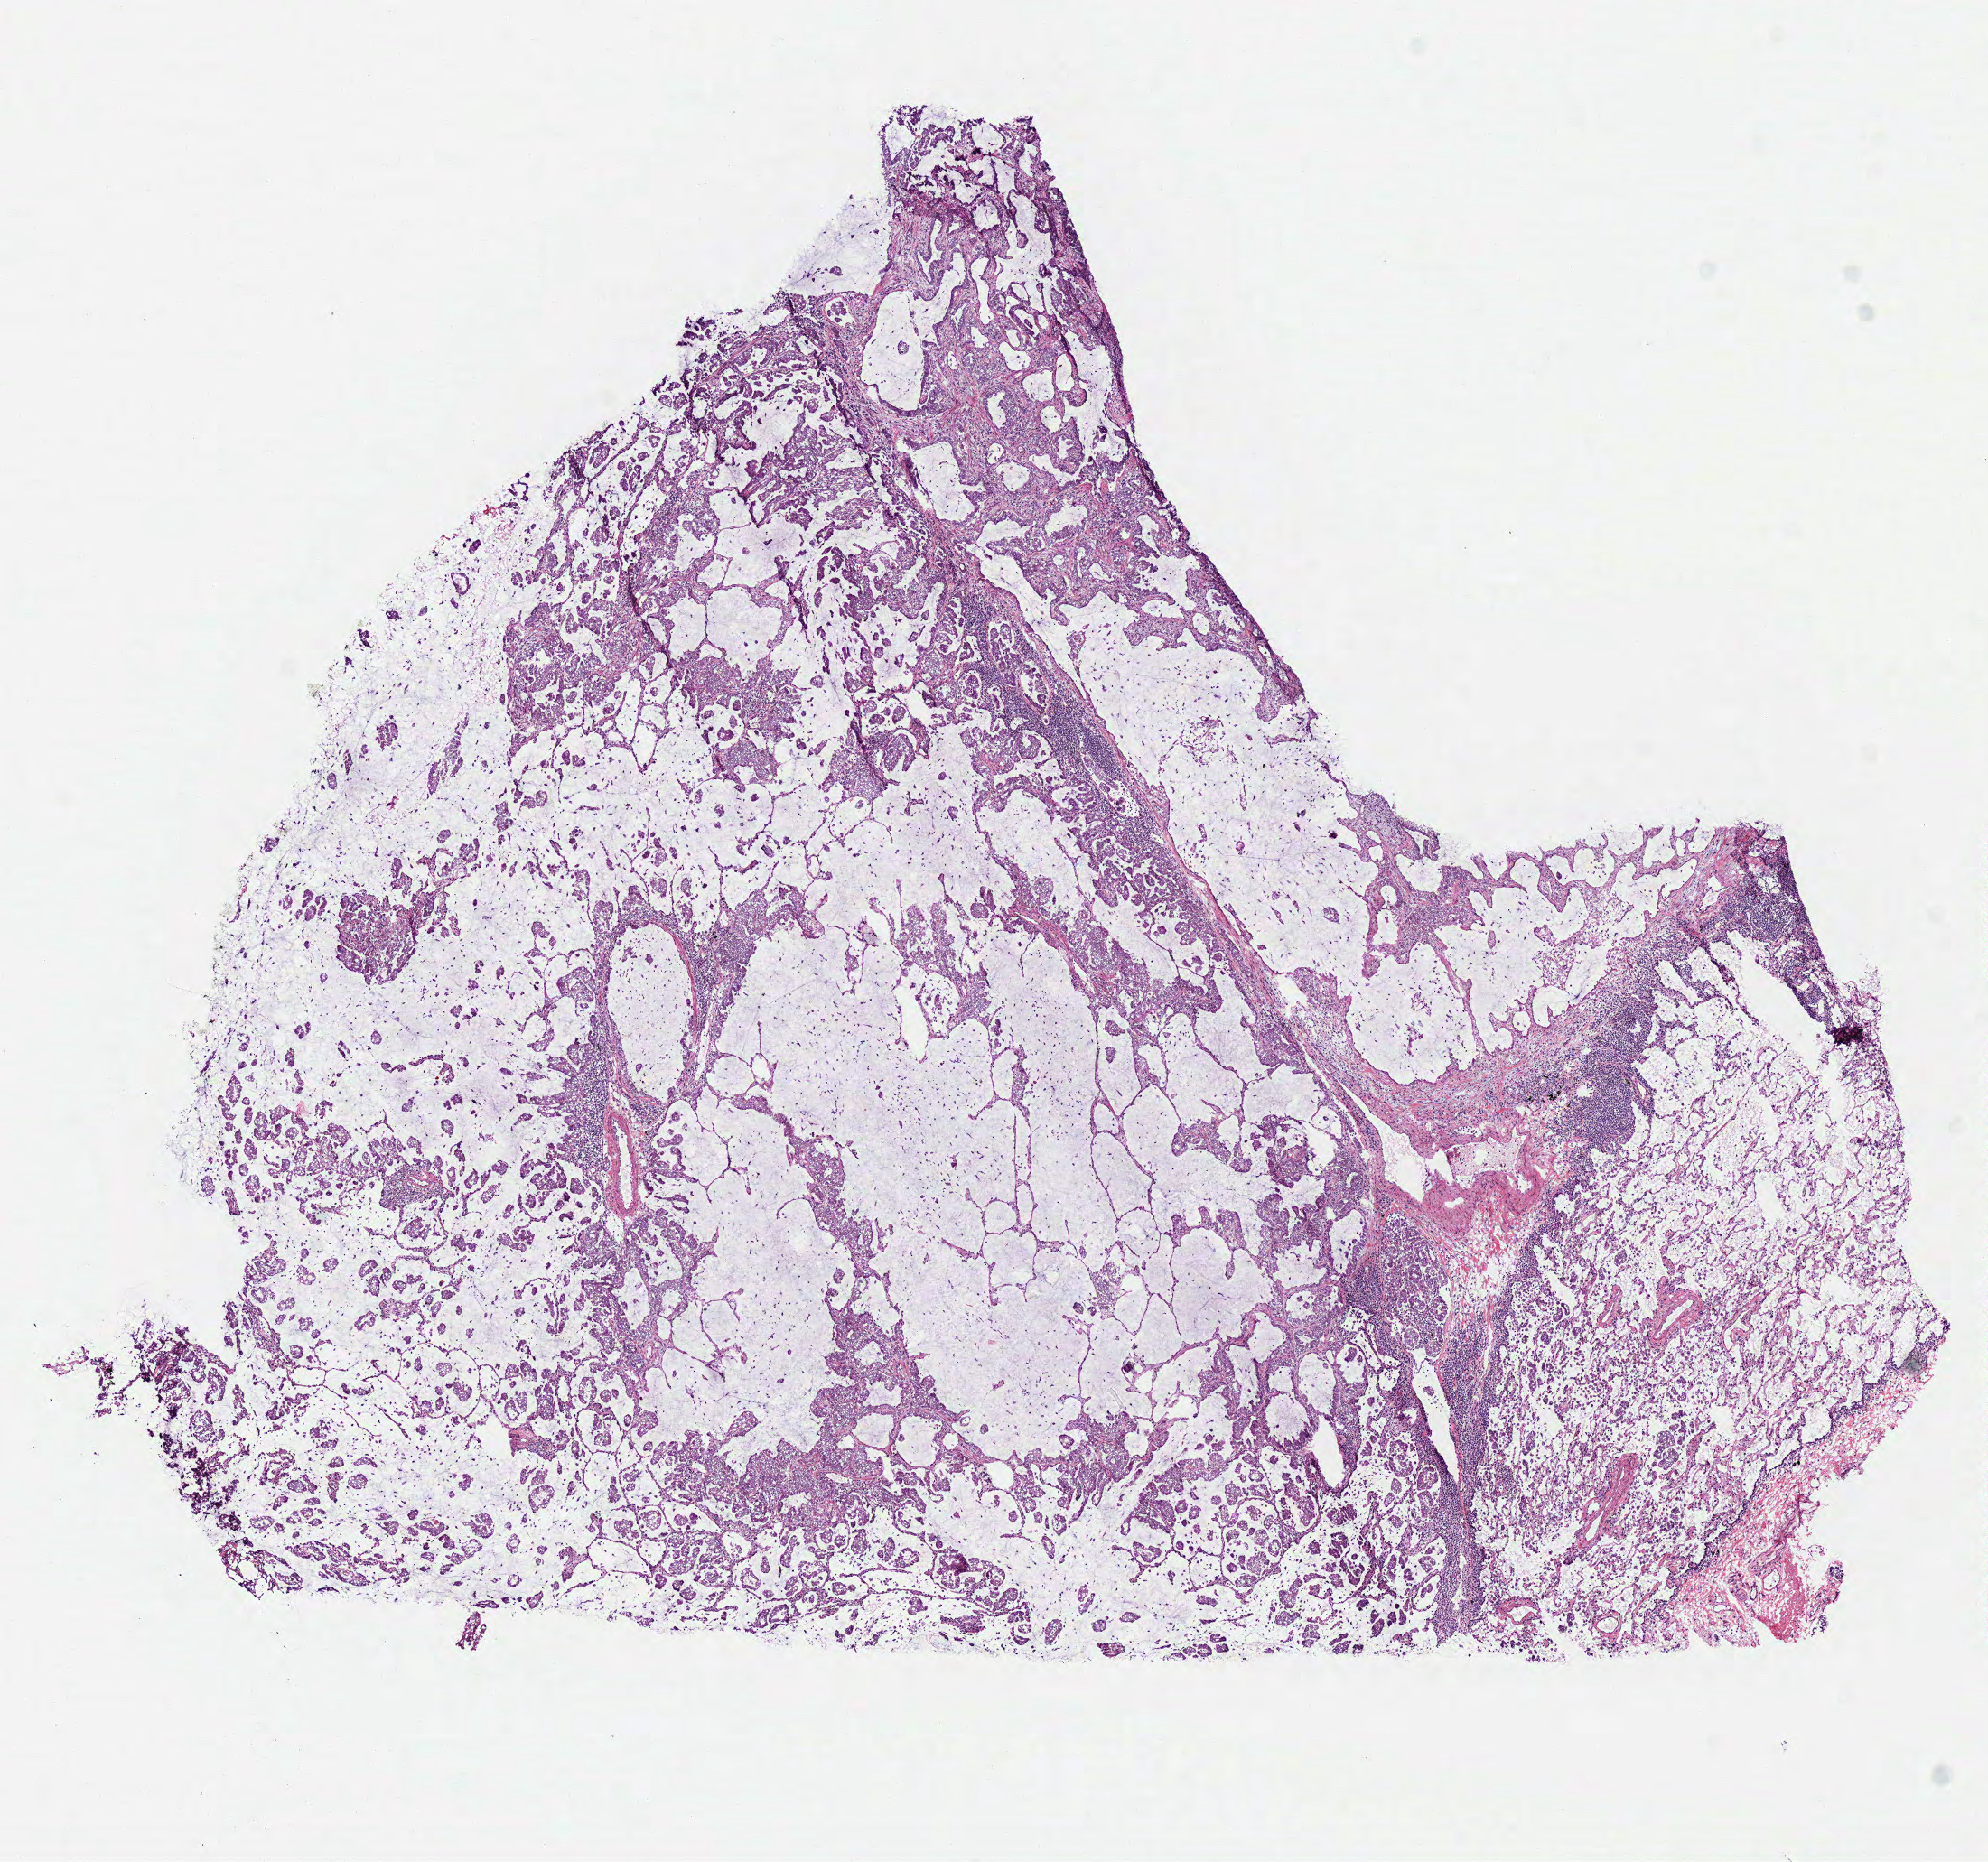
Whole-slide histology image, H&E-stained — low-resolution overview of the scanned area, about 8.7 x 8.1 mm. Frozen section from the bottom of the tissue portion. Lung, primary tumour sample. Male, age 61 years at initial diagnosis. Pathologist review of this section (percent, as recorded): tumour cells 85%, tumour nuclei 60%, normal cells 0%, stromal cells 15%, necrosis 0%.
AJCC pathologic stage: IV. Laterality: right. Pathologic diagnosis: Adenocarcinoma with mixed subtypes (lower lobe, lung).